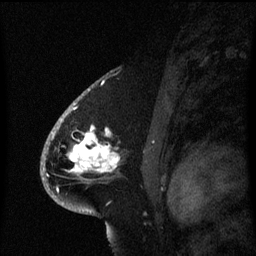
Breast MRI (dynamic contrast-enhanced), one sagittal slice. Slice 42 of 60 in the series (ordered by position). Dynamic contrast-enhanced series, image 2 of 3 at this slice position (ordered by acquisition). 1.5 T. TE 4.2 ms, TR 8.4 ms. 2.1 mm slice thickness. 256 × 256 image matrix. Female patient, age 53 years. Case-level facts recorded for this patient, not image findings: setting: breast cancer imaged before/during neoadjuvant chemotherapy; receptor status: HR-positive, HER2-negative.
Outlined on this slice (semi-automatically segmented with operator editing):
- analysis volume of interest (the breast-tissue region the enhancement analysis was run in; not a lesion): bounding box [x1, y1, x2, y2] px = [49, 108, 121, 201]
- tumour enhancement mask (voxels above the 70 % enhancement threshold inside the analysis volume of interest): [53, 120, 120, 173]